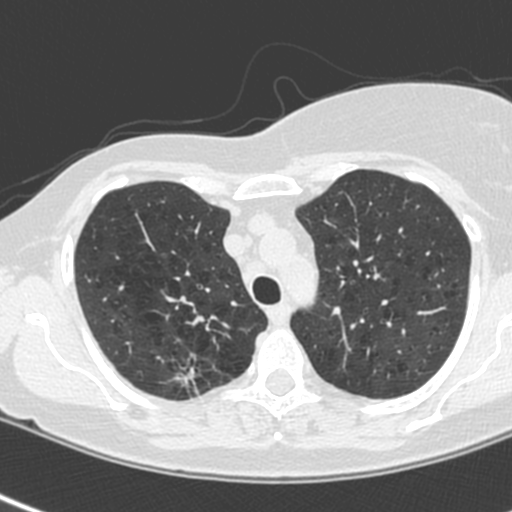
Low-dose screening chest CT, axial slice; baseline annual screen; lung window (W 1500 / L -600 HU); 1.3 mm slice thickness; slice 43 of 214 in the series. Female, age 64 years at enrolment.
- Lesion marked by an expert reader, bounding box (x1, y1, x2, y2) in pixels: (164, 355, 221, 406).
- The exam's reader record, not a measurement of the box and not confirmed to be the same lesion: non-calcified nodule or mass ≥4 mm, right upper lobe, 13 × 10 mm, spiculated (stellate) margins, soft tissue attenuation.
- Official screen result: positive, change unspecified: nodule(s) >= 4 mm or enlarging nodule(s), mass(es), or other non-specific abnormalities suspicious for lung cancer.
- Lung cancer was diagnosed 21 days after this screen: adenocarcinoma, NOS, right upper lobe, poorly differentiated (G3), stage IIIB (AJCC 6th edition), 20 mm at pathology.